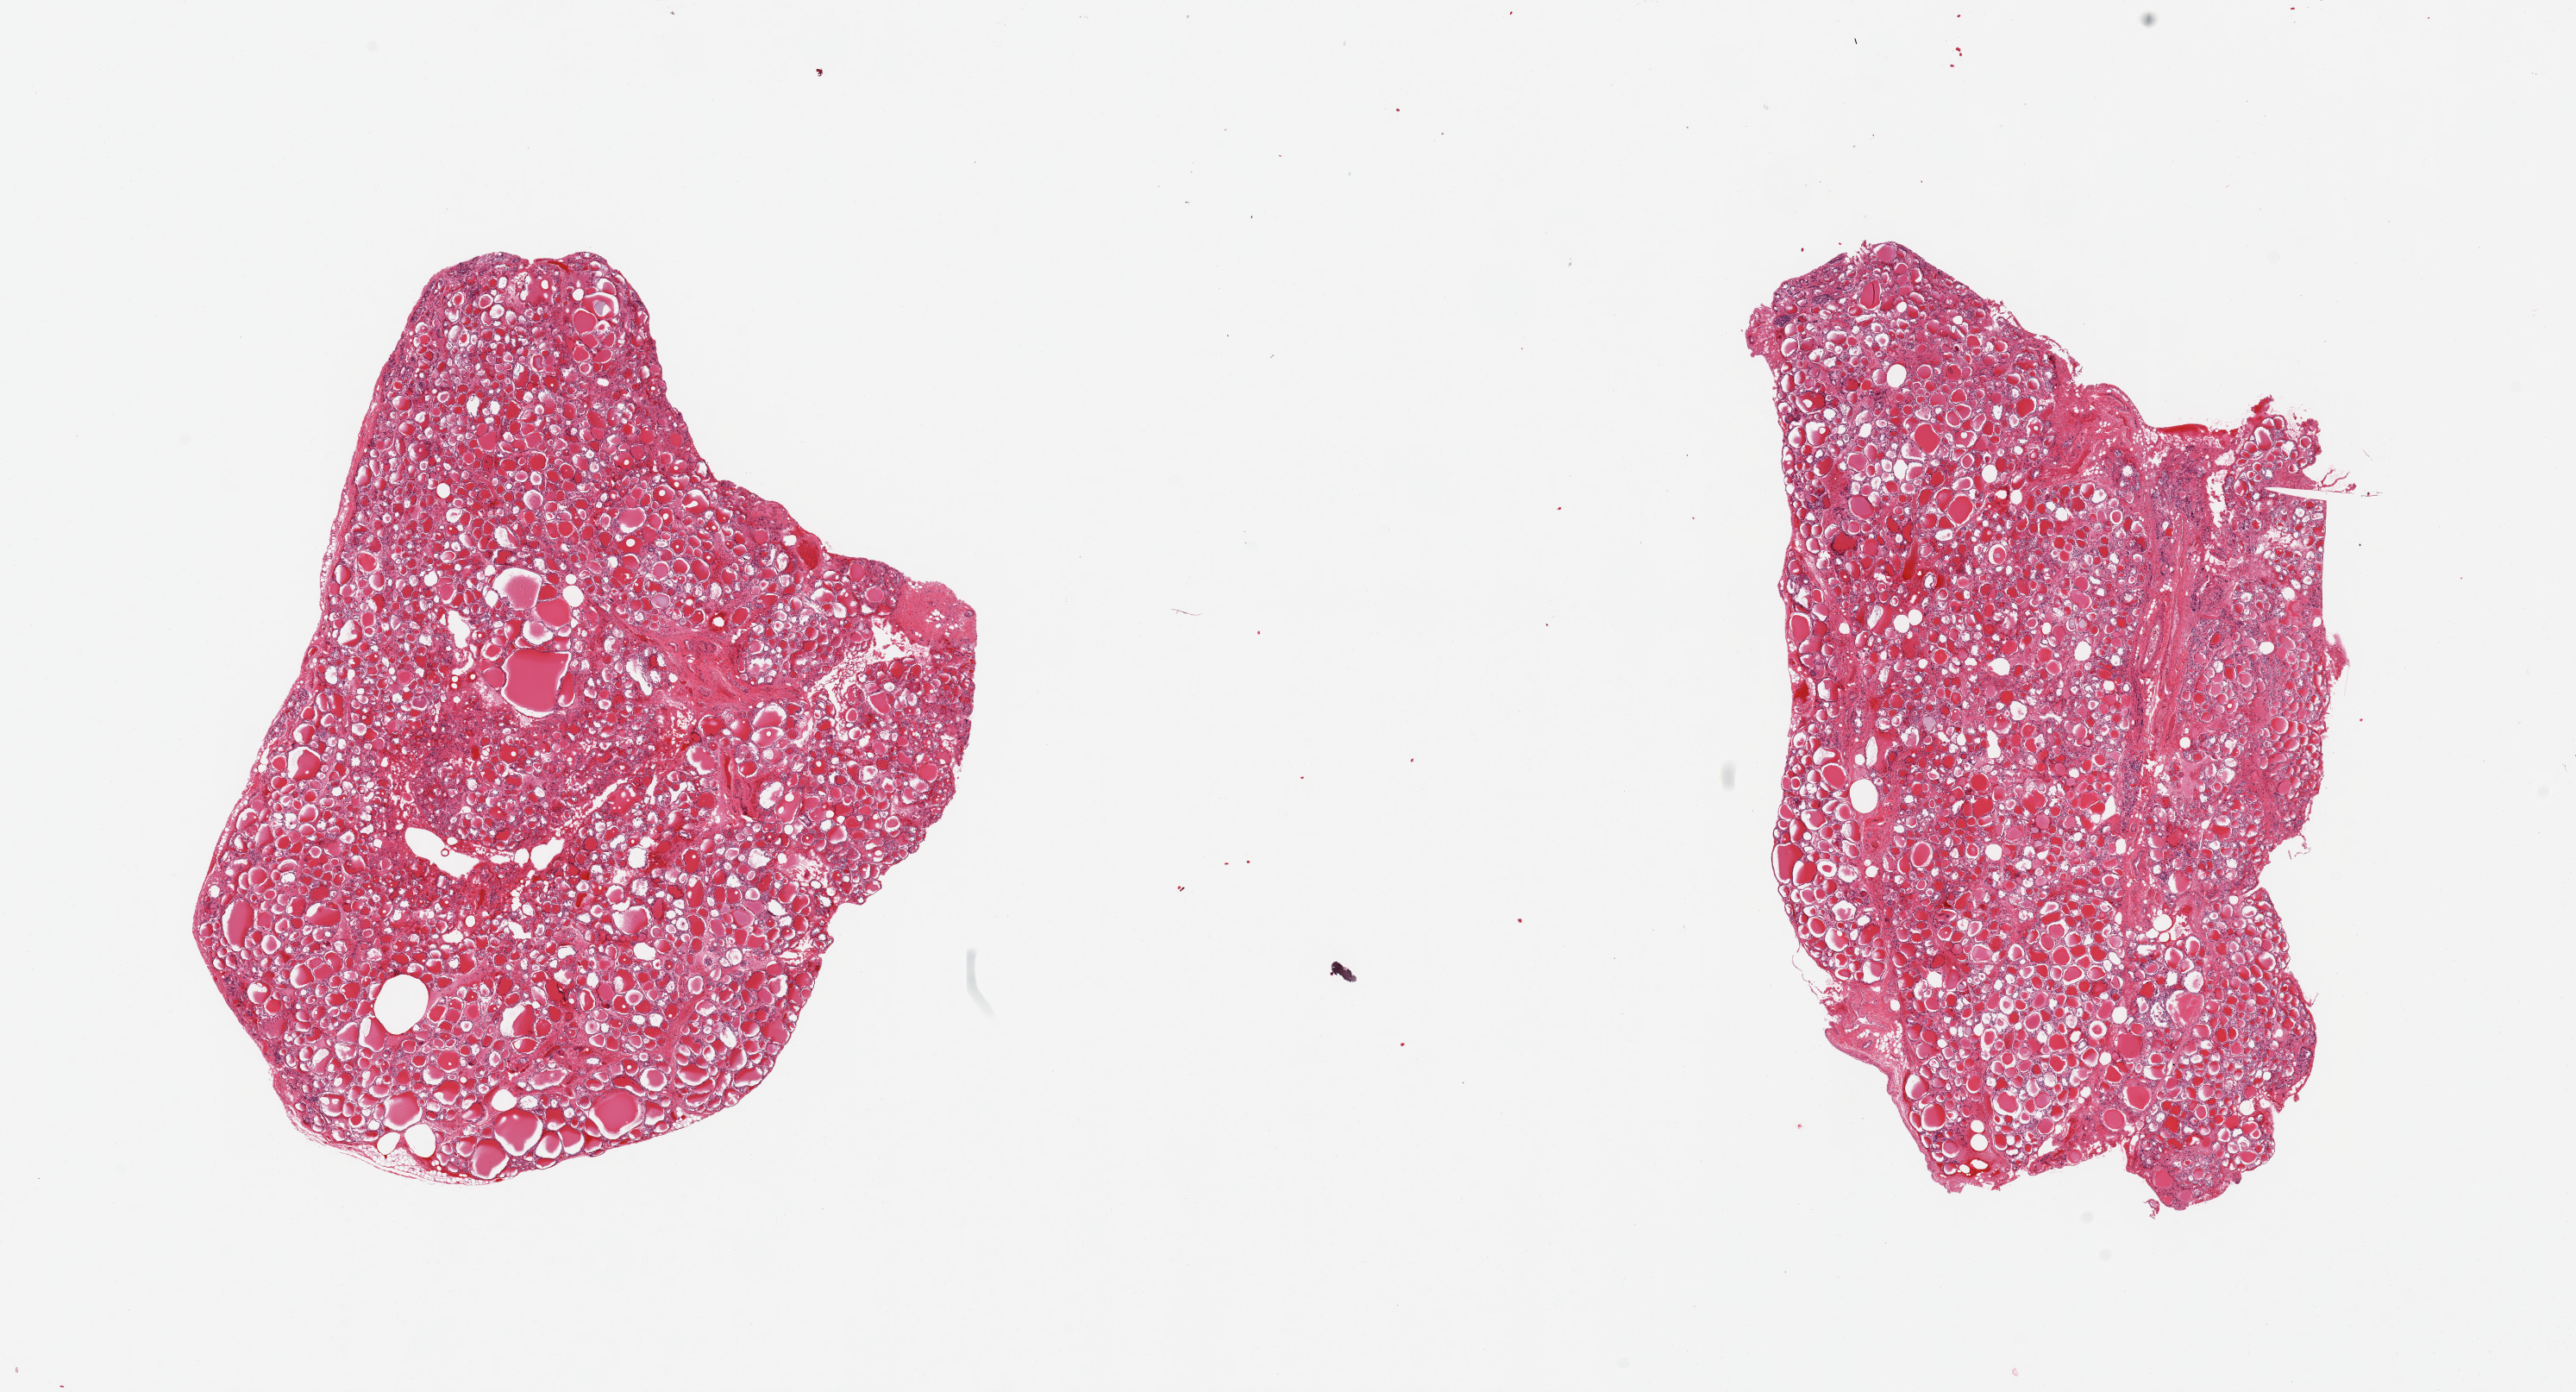
Whole-slide image, haematoxylin and eosin stain, a low-resolution overview of the entire scanned area, about 23.6 x 12.8 mm. PAXgene-fixed paraffin-embedded (PFPE) section. Section of thyroid (target tissue). Donor tissue sample. Donor sex: female.
Pathologist's review note for this sample: 2 pieces, no abnormalities.